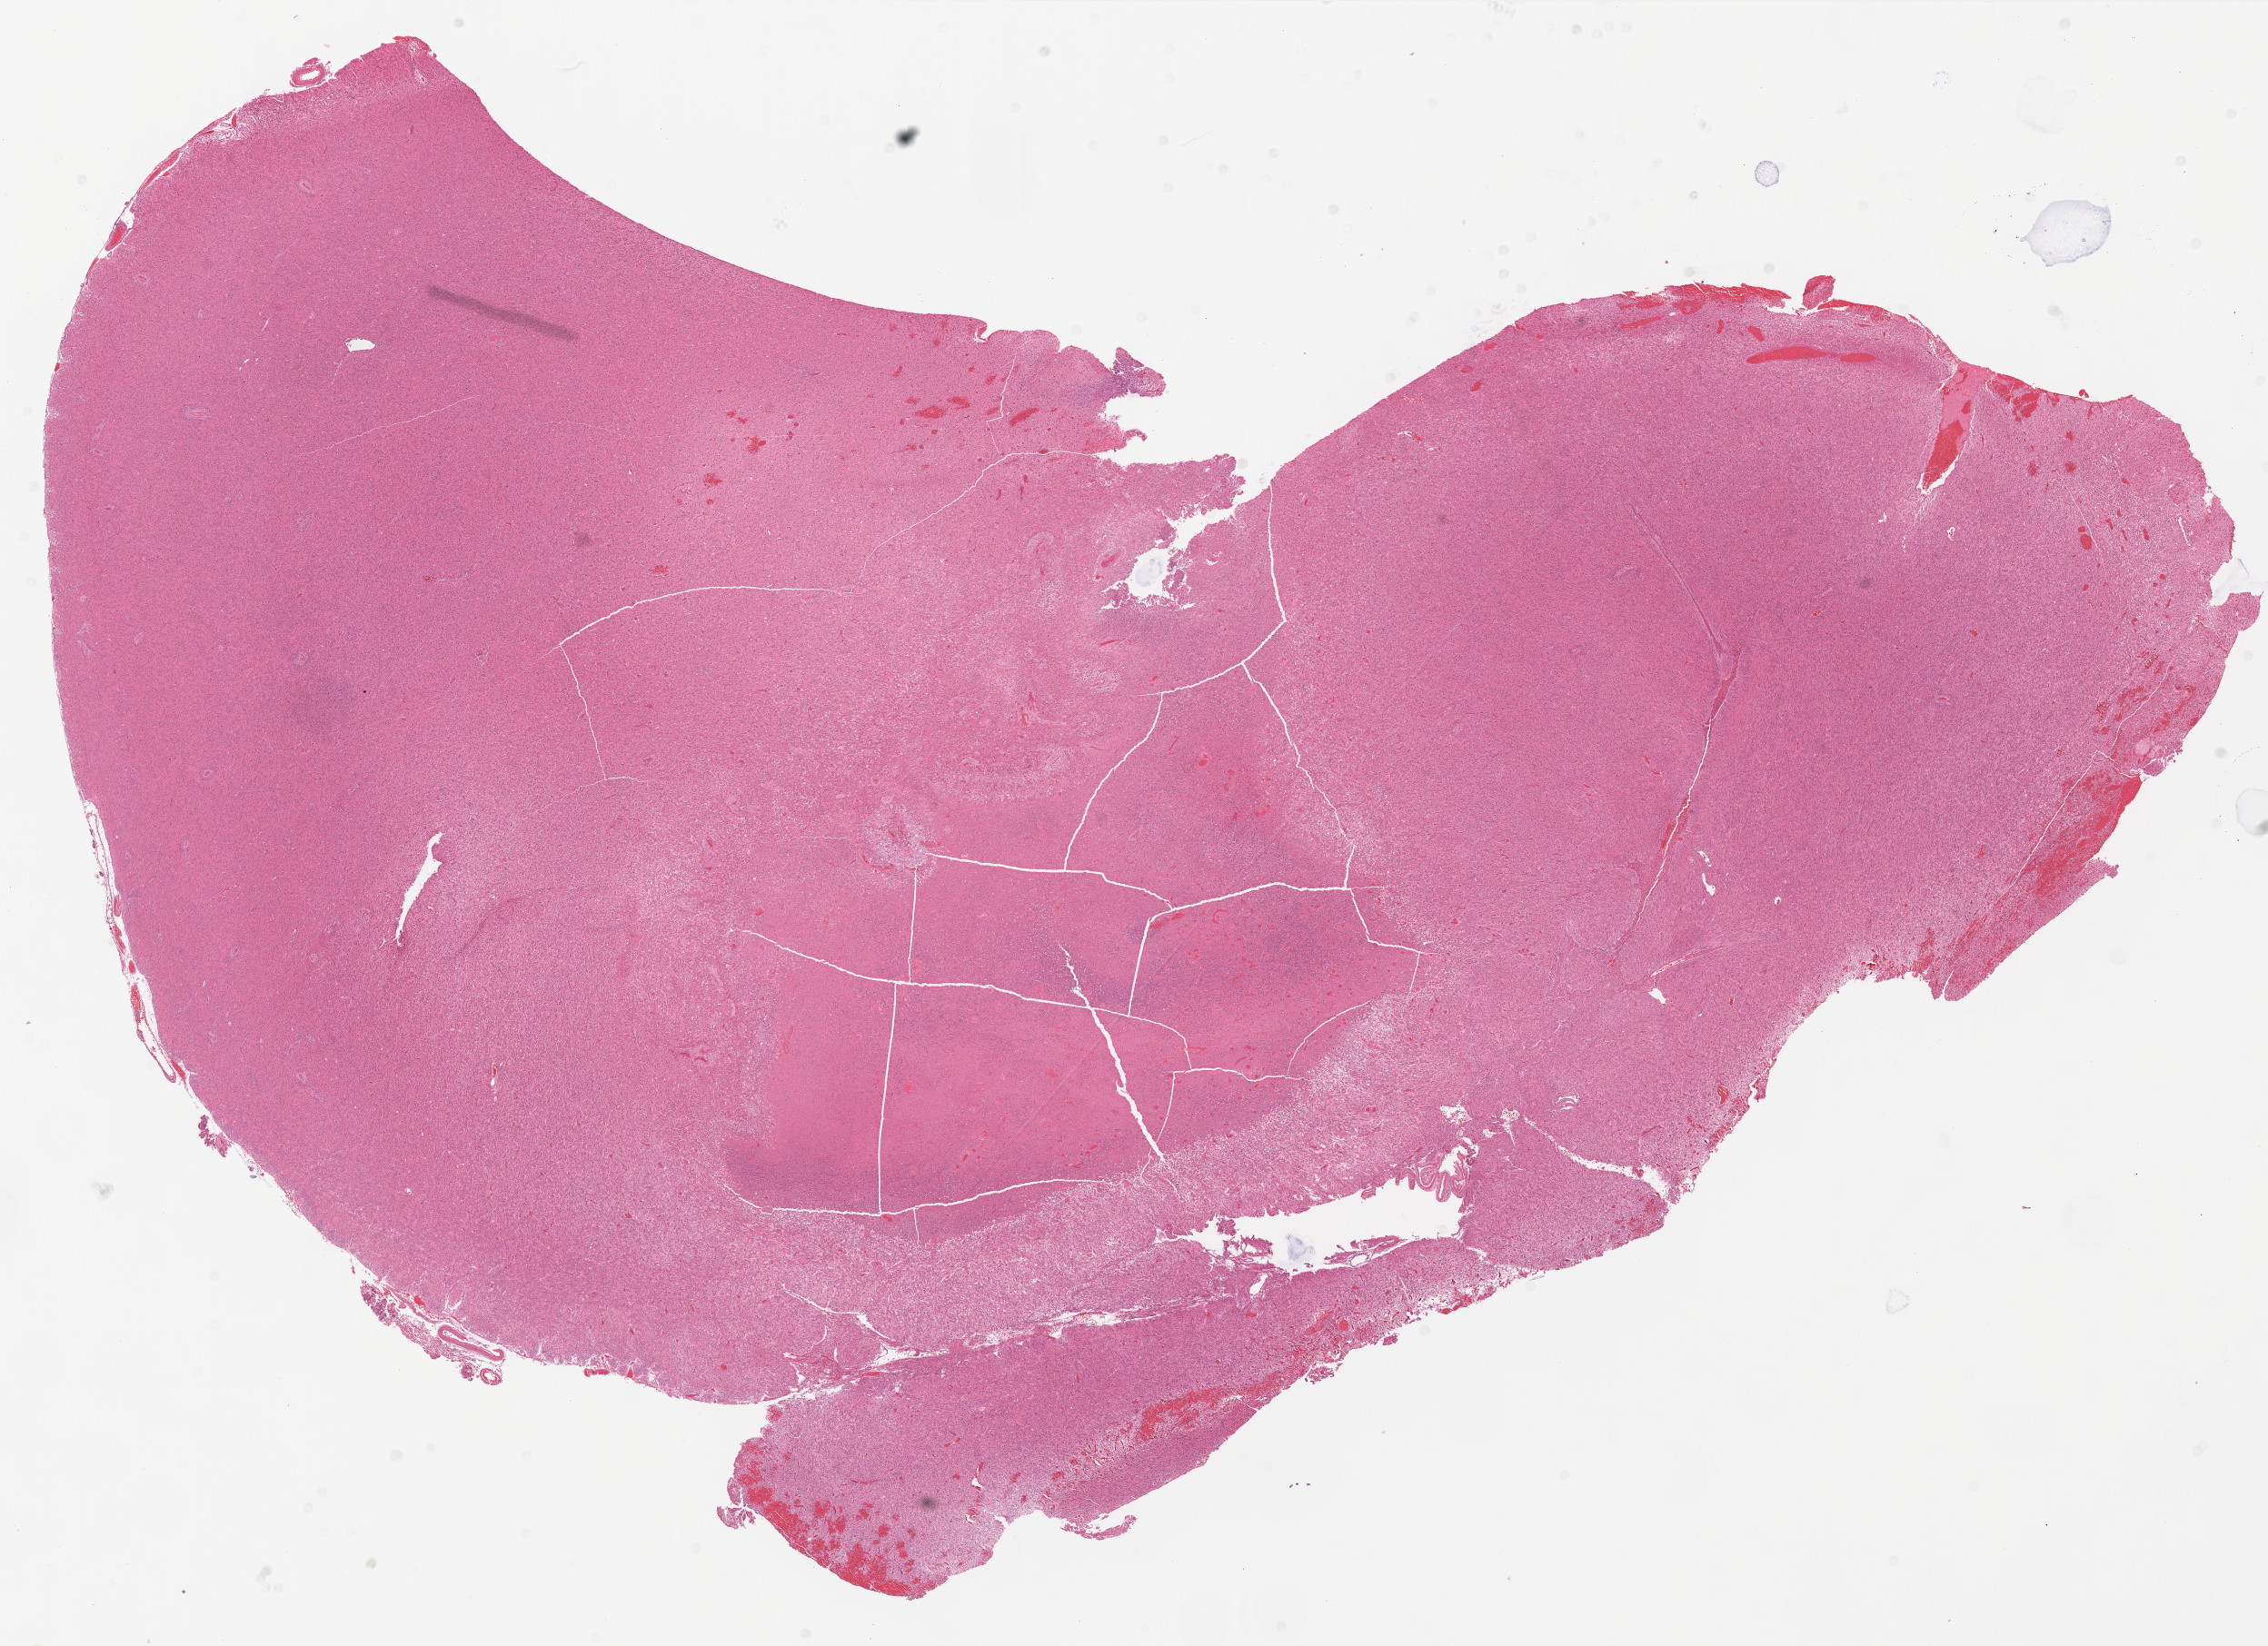
Digitized H&E-stained tissue section (whole slide) — a low-resolution overview of the entire scanned area, about 20.0 x 14.5 mm; formalin-fixed paraffin-embedded (FFPE) diagnostic section; sample: primary tumour, brain. Male, age 68 years at initial diagnosis.
- diagnosis: Glioblastoma